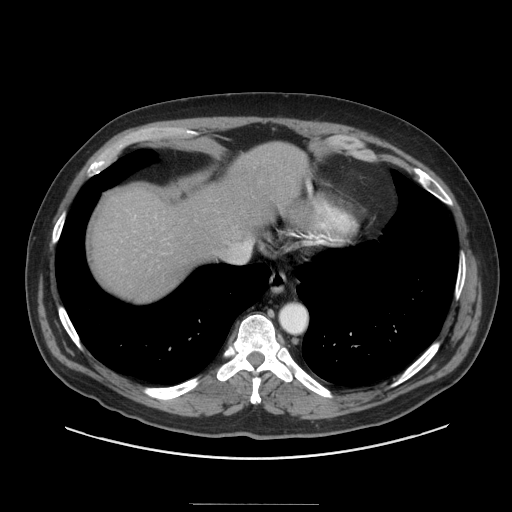
Contrast-enhanced abdominal CT (liver protocol), one axial slice; position 81 of 91 along the scan axis; 140 kVp; soft-tissue window (W 400 / L 40 HU); 2.5 mm slice thickness; 512 × 512 image matrix. Case-level facts recorded for this patient, not image findings: diagnosis: hepatocellular carcinoma (patient treated with transarterial chemoembolisation; whether this scan precedes or follows treatment is not stated here); TNM stage (as recorded): Stage-I; Child-Pugh class: A; tumour size: 4 cm.
Outlined on this slice (semi-automatically segmented with operator editing):
- liver parenchyma outside the tumour (the mass and vessels are separate outlines, so this box may not span the whole liver): bounding box [x1, y1, x2, y2] px = [92, 142, 306, 302]